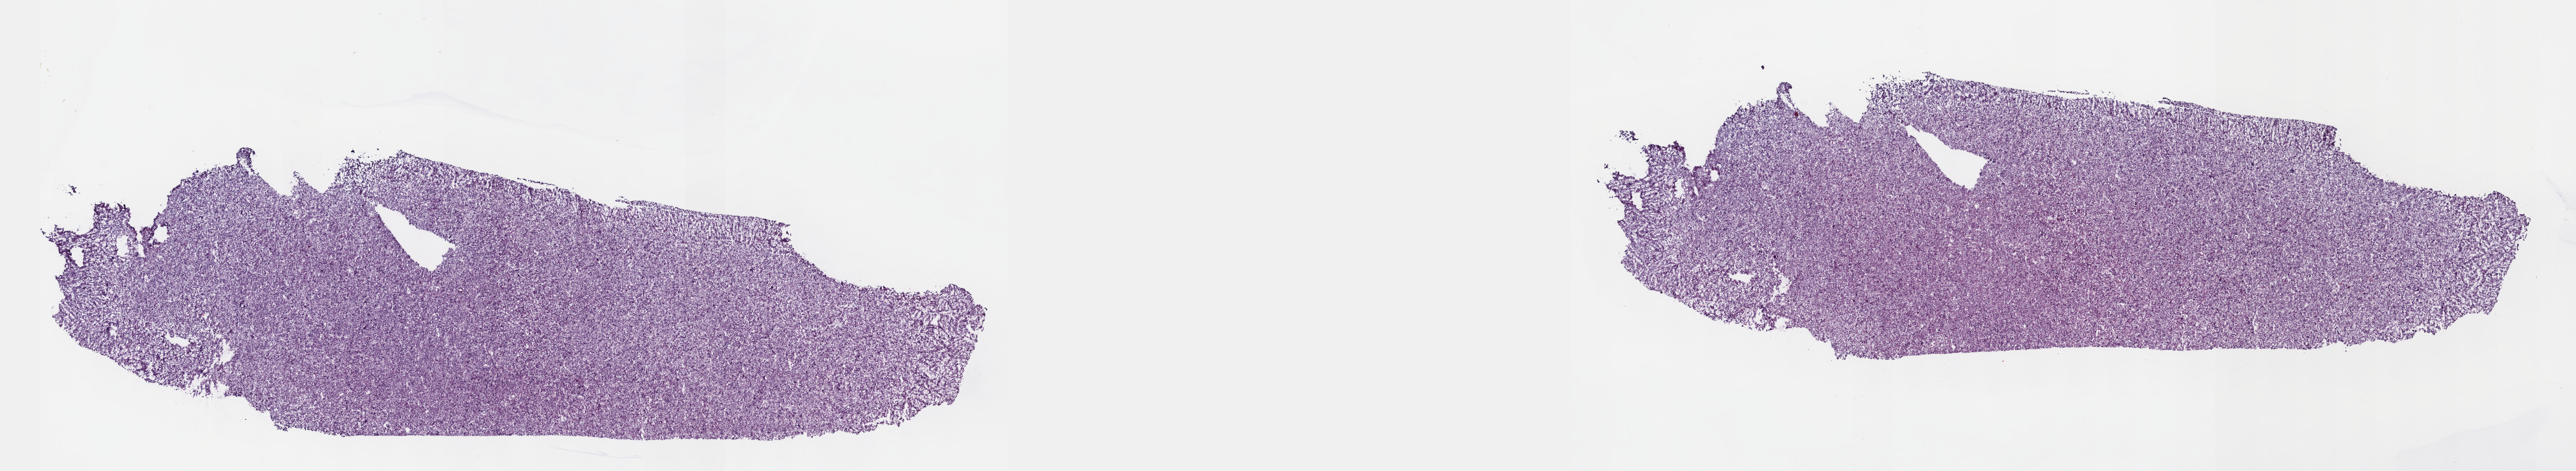
Digitized Hematoxylin and eosin (H&E) stained tissue section (whole slide) — whole scanned area (about 32.2 x 5.9 mm) shown as a low-resolution overview, frozen section, primary tumour sample from the connective, subcutaneous and other soft tissues. Patient: female, age at initial diagnosis 65 years. Composition of this section per pathologist review: tumour cells 100%, tumour nuclei 80%.
Pathologic diagnosis: Malignant fibrous histiocytoma (connective, subcutaneous and other soft tissues of lower limb and hip).